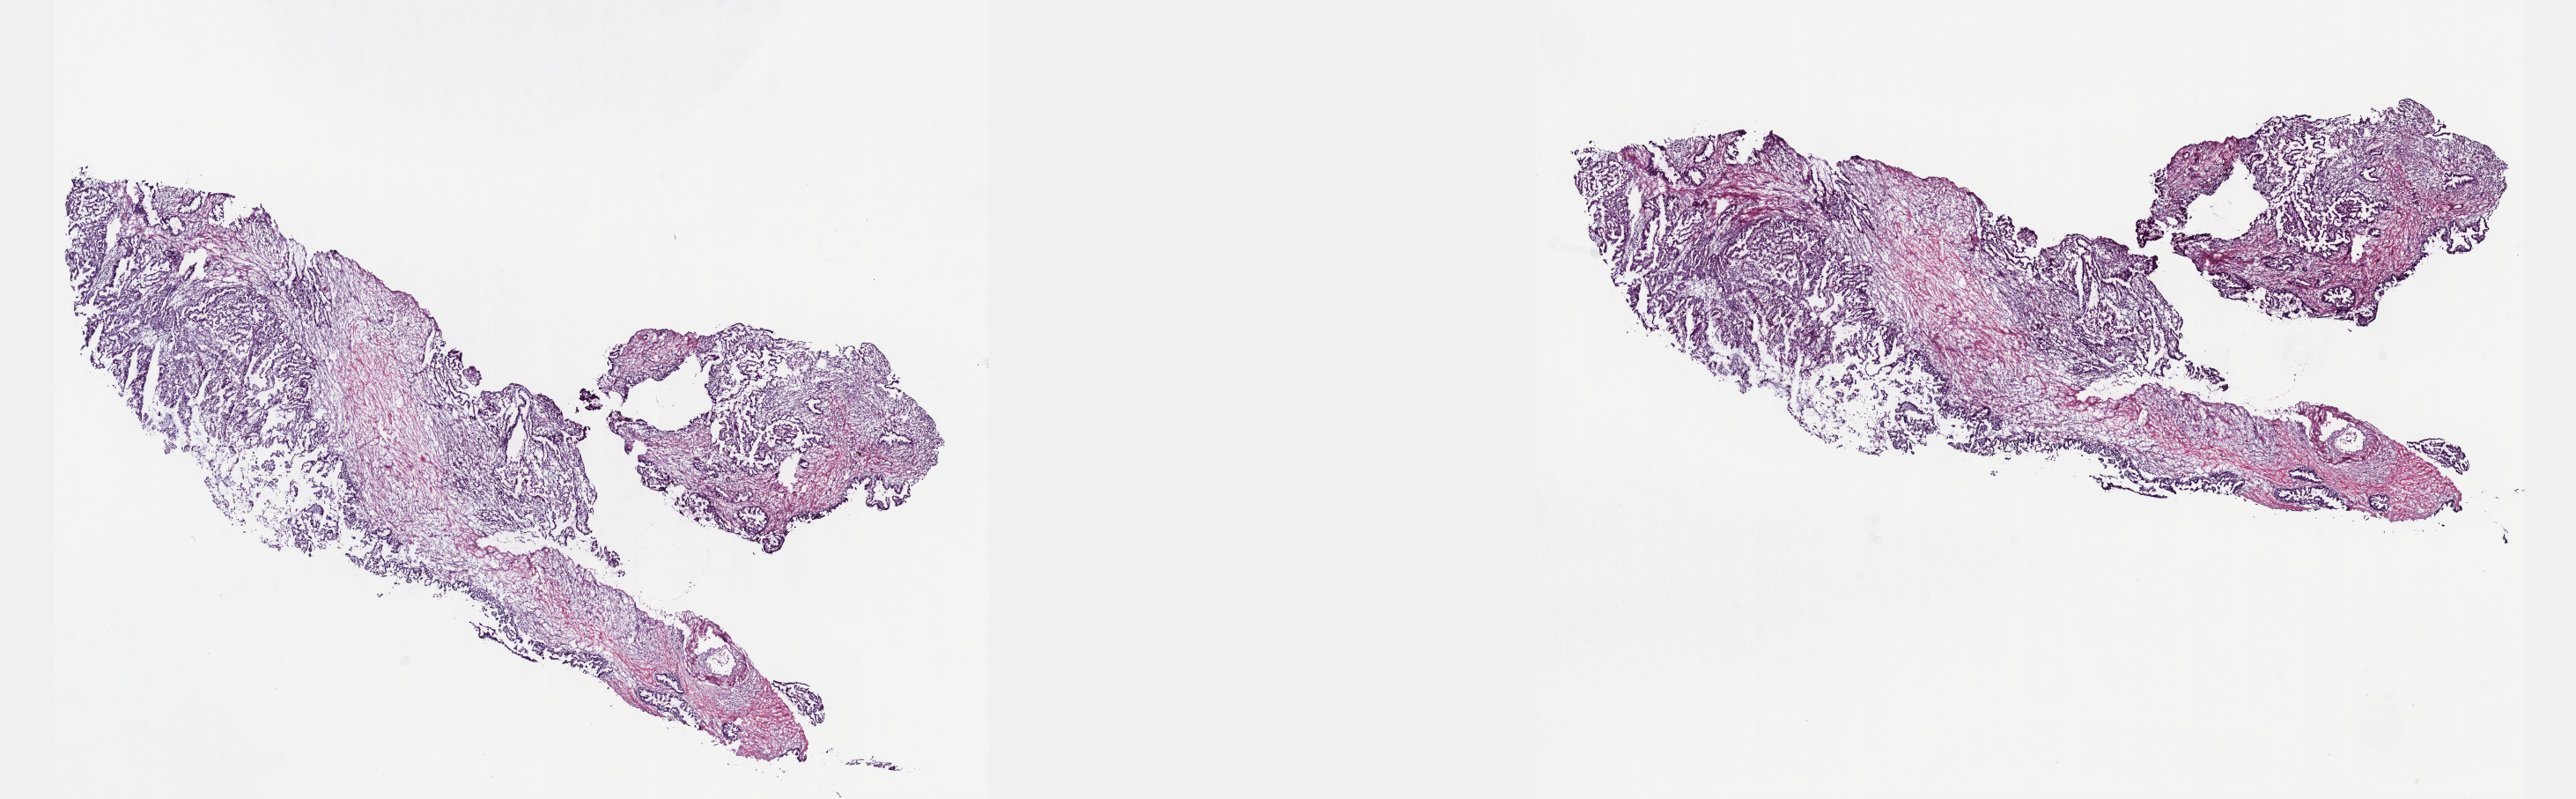
Whole-slide histology image, Hematoxylin and eosin (H&E) stained — a low-resolution overview of the entire scanned area, about 23.6 x 7.3 mm. Frozen section from the top of the tissue portion. Pancreas, primary tumour sample. Patient: female, age at initial diagnosis 41 years. Histologic grade: G2 (moderately differentiated). Pathologist review of this section (percent, as recorded): tumour cells 60%, tumour nuclei 60%, normal cells 0%, stromal cells 35%, necrosis 5%. Inflammatory infiltration, as recorded: lymphocyte infiltration 40%, monocyte infiltration 20%, neutrophil infiltration 20%.
TNM: T3 N0 MX. Histologic diagnosis: Infiltrating duct carcinoma, NOS (head of pancreas). AJCC pathologic stage: IIA.